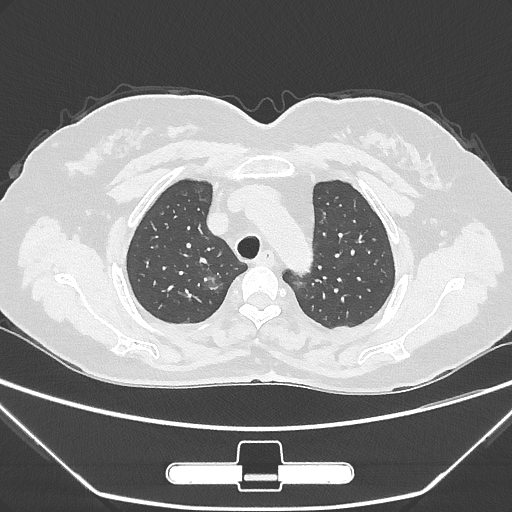
Chest CT, one axial slice; slice 225 of 275 in the series (ordered by position); reconstruction kernel IMR1,SharpPlus; 120 kVp; lung window (W 1500 / L -600 HU); 1 mm slice thickness; 512 × 512 image matrix, field of view 356 × 356 mm. Patient: female, 63 years. Case-level facts recorded for this patient, not image findings: clinical TNM (as recorded): T1a N0 M0.
Structures marked on this image (rectangle marked by the reading radiologist):
- lung tumour (recorded histology: adenocarcinoma): bounding box <197,267,227,295> (left, top, right, bottom; pixels)